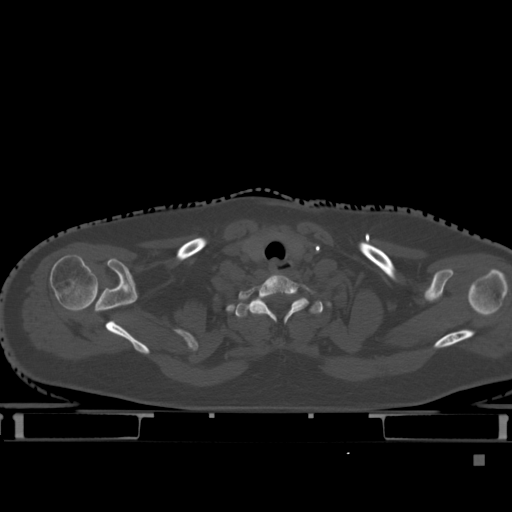
CT including the spine, one axial slice; slice 377 of 495 in the series (ordered by position); bone window (W 1800 / L 400 HU); 1.5 mm slice thickness; 512 × 512 image matrix, field of view 404 × 404 mm. Patient: female, 33 years. From the clinical record (not read from this slice): primary cancer: breast; vertebrae with lytic lesions (as recorded): T1.
Structures marked on this image (semi-automatically segmented with operator editing):
- T1 vertebra: bounding box (x1, y1, x2, y2) in pixels: (235, 298, 323, 322)